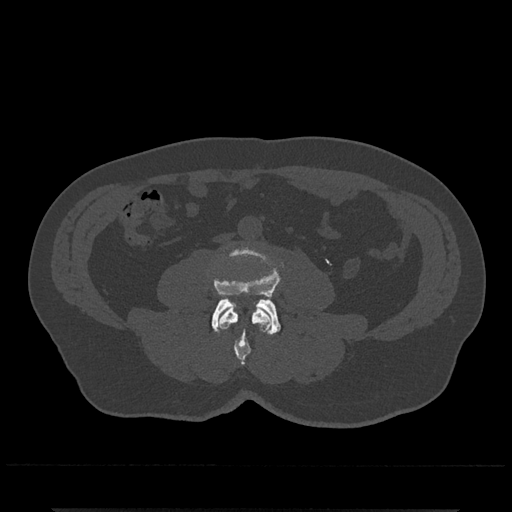
CT including the spine, one axial slice; slice 185 of 797 in the series (ordered by position); reconstruction kernel Br40s/3; 120 kVp; bone window (W 1800 / L 400 HU); 512 × 512 image matrix, field of view 393 × 393 mm. Patient: male, 67 years. From the clinical record (not read from this slice): primary cancer: prostate.
Structures marked on this image (semi-automatic segmentation, software-assisted and operator-edited):
- L3 vertebra: bounding box (x1, y1, x2, y2) in pixels: (218, 307, 272, 365)
- L4 vertebra: (212, 249, 281, 335)